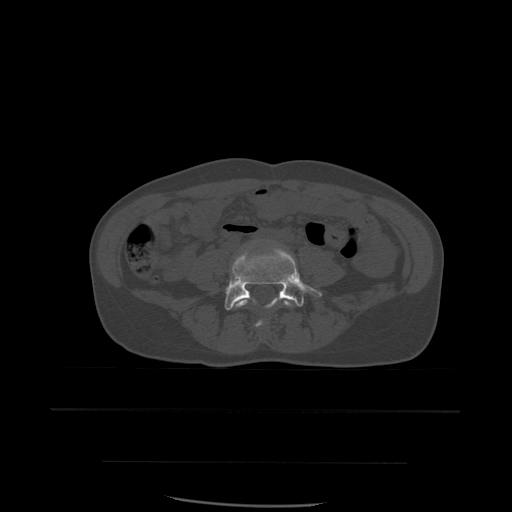
CT including the spine, one axial slice. Position 156 of 574 along the scan axis. Bone window (W 1800 / L 400 HU). 1.25 mm slice thickness. 512 × 512 image matrix, field of view 392 × 392 mm. Patient age 48 years. From the clinical record (not read from this slice): primary cancer: lung; vertebrae with lytic lesions (as recorded): T11.
Structures marked on this image (semi-automatic segmentation, software-assisted and operator-edited):
- L4 vertebra: bounding box (x1, y1, x2, y2) in pixels: (231, 291, 294, 329)
- L5 vertebra: (225, 248, 322, 310)